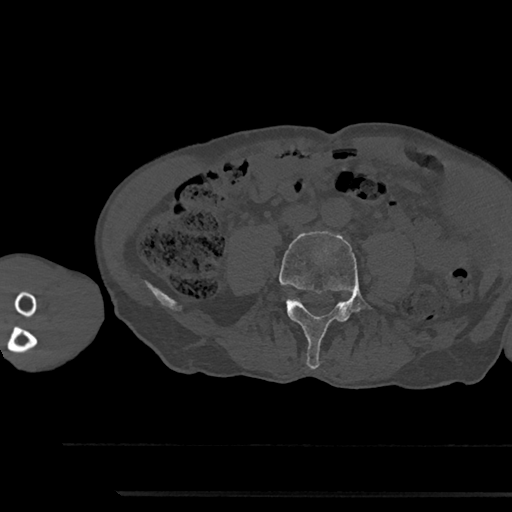
CT including the spine, one axial slice; position 408 of 797 along the scan axis; bone window (W 1800 / L 400 HU); 0.5 mm slice thickness; 512 × 512 image matrix. Male patient, age 79 years. From the clinical record (not read from this slice): primary cancer: prostate.
Annotated regions visible in this slice (semi-automatically segmented with operator editing):
- L4 vertebra: box from (x=279, y=231) to (x=368, y=369) px